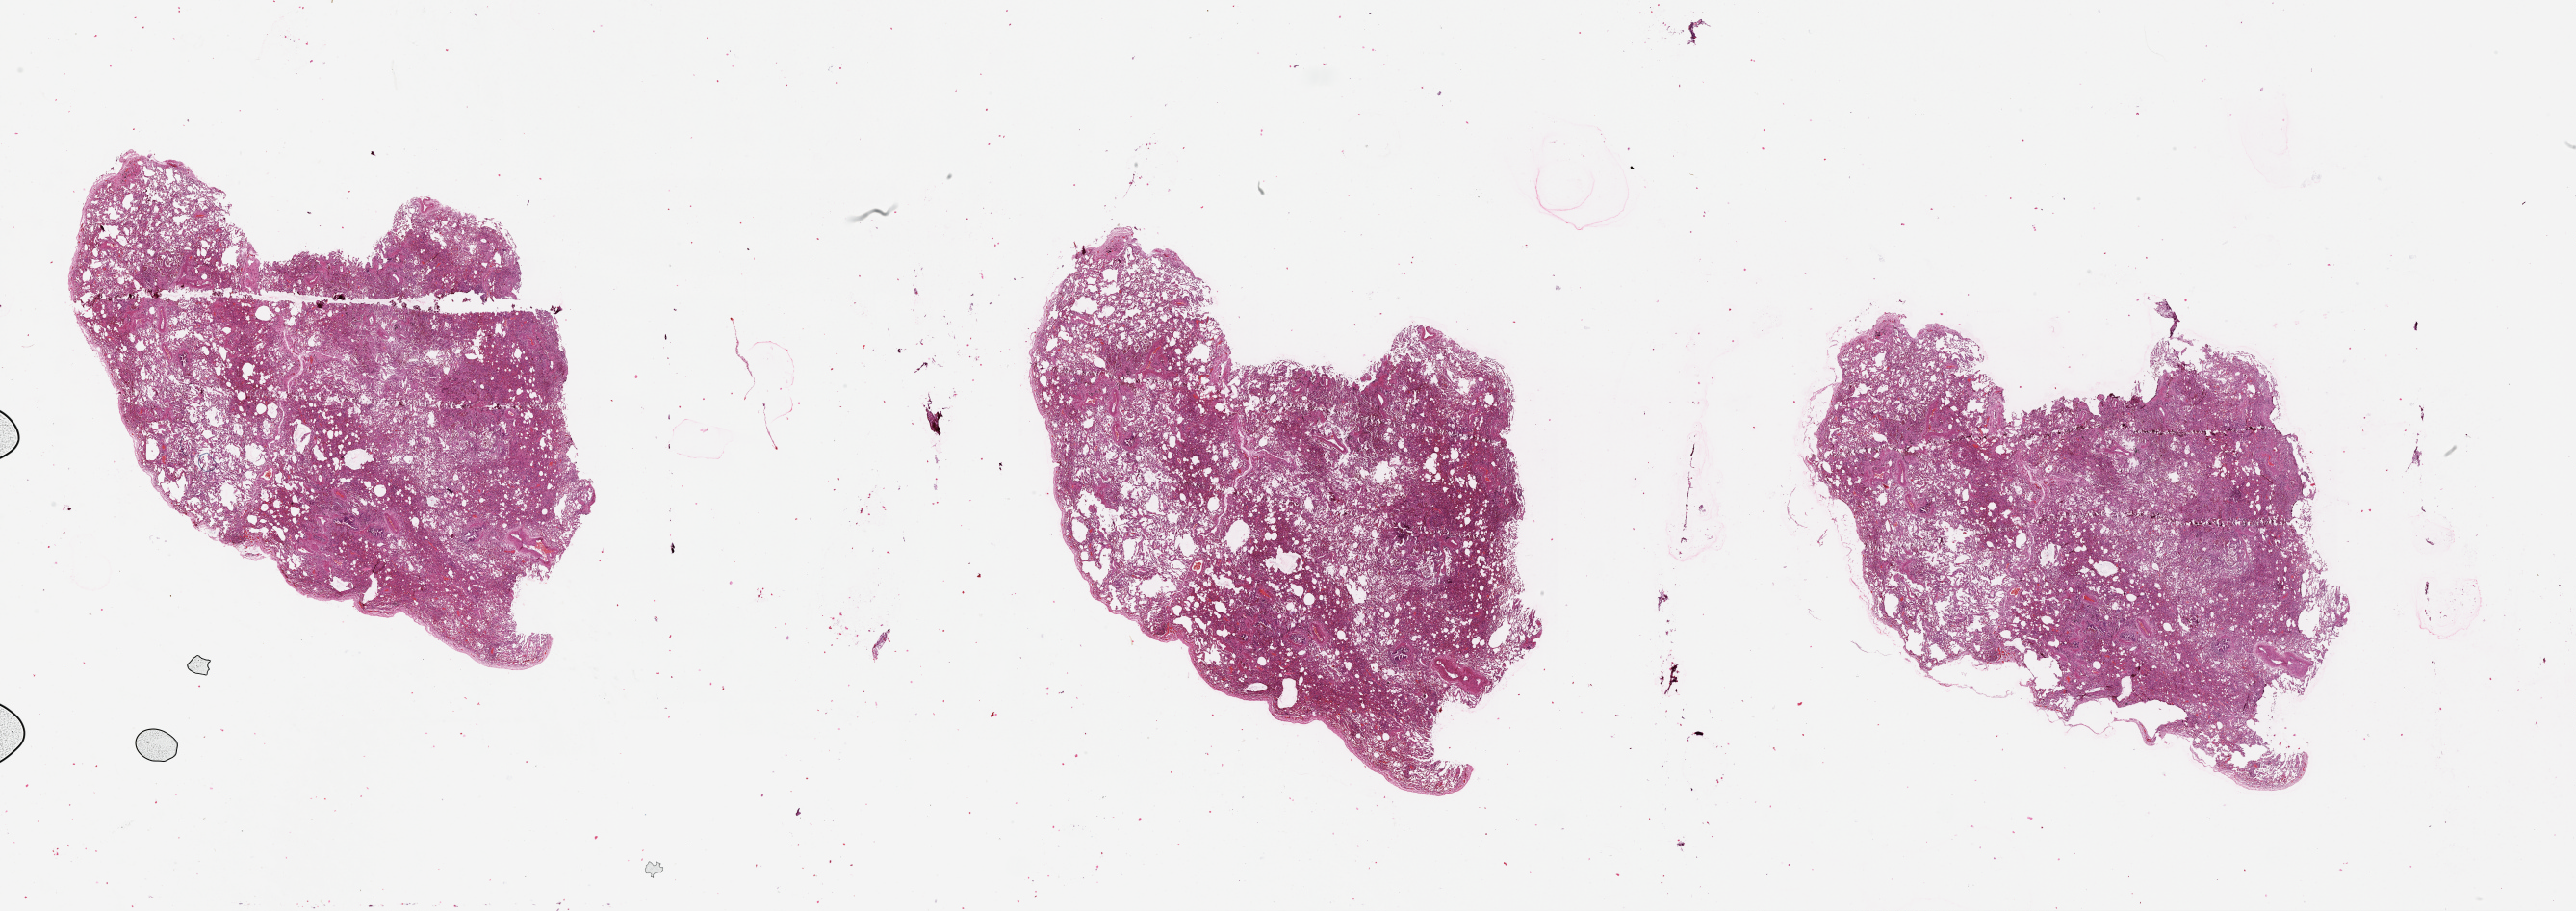
Whole-slide histology image, Hematoxylin and eosin (H&E) stained, shown as a low-resolution overview of the whole scanned area (about 43.1 x 15.2 mm, acquisition: 20x scan); lung, tissue type not recorded.
Patient diagnosis (cohort enrolment): lung adenocarcinoma (lung).